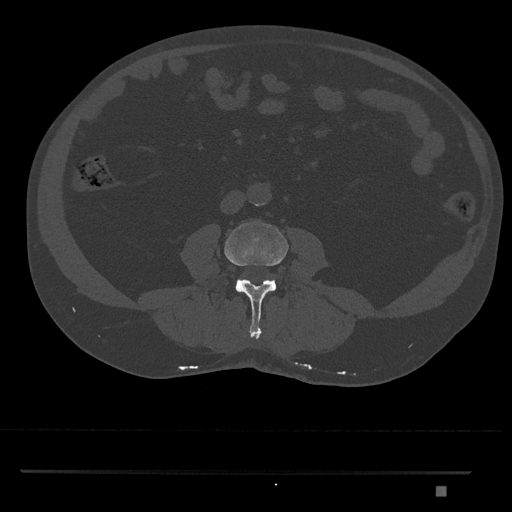
CT including the spine, one axial slice; reconstruction kernel Br40s/3; 120 kVp; bone window (W 1800 / L 400 HU); 512 × 512 image matrix. Patient: male, 65 years. From the clinical record (not read from this slice): primary cancer: prostate.
Outlined on this slice (semi-automatically segmented with operator editing):
- L3 vertebra: bounding box [x1, y1, x2, y2] px = [224, 221, 289, 339]